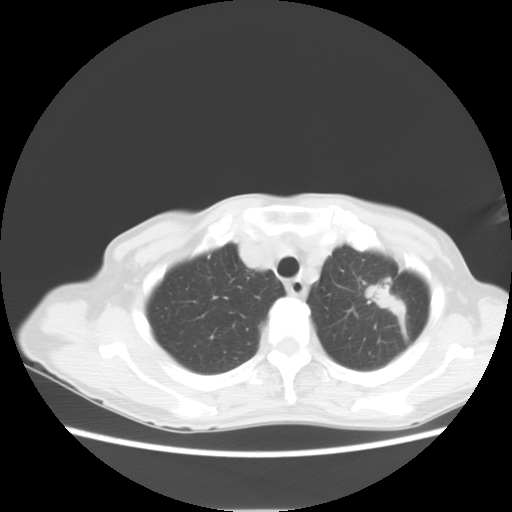
Chest CT, one axial slice. Position 8 of 11 along the scan axis. Reconstruction kernel STANDARD. 120 kVp. Lung window (W 1500 / L -600 HU). 5 mm slice thickness. 512 × 512 image matrix, field of view 350 × 350 mm. Patient: female, 71 years. Case-level facts recorded for this patient, not image findings: clinical TNM (as recorded): T2 N0 M0.
Annotated regions visible in this slice (rectangle marked by the reading radiologist):
- lung tumour (recorded histology: adenocarcinoma): bounding box [x1, y1, x2, y2] px = [365, 280, 409, 324]